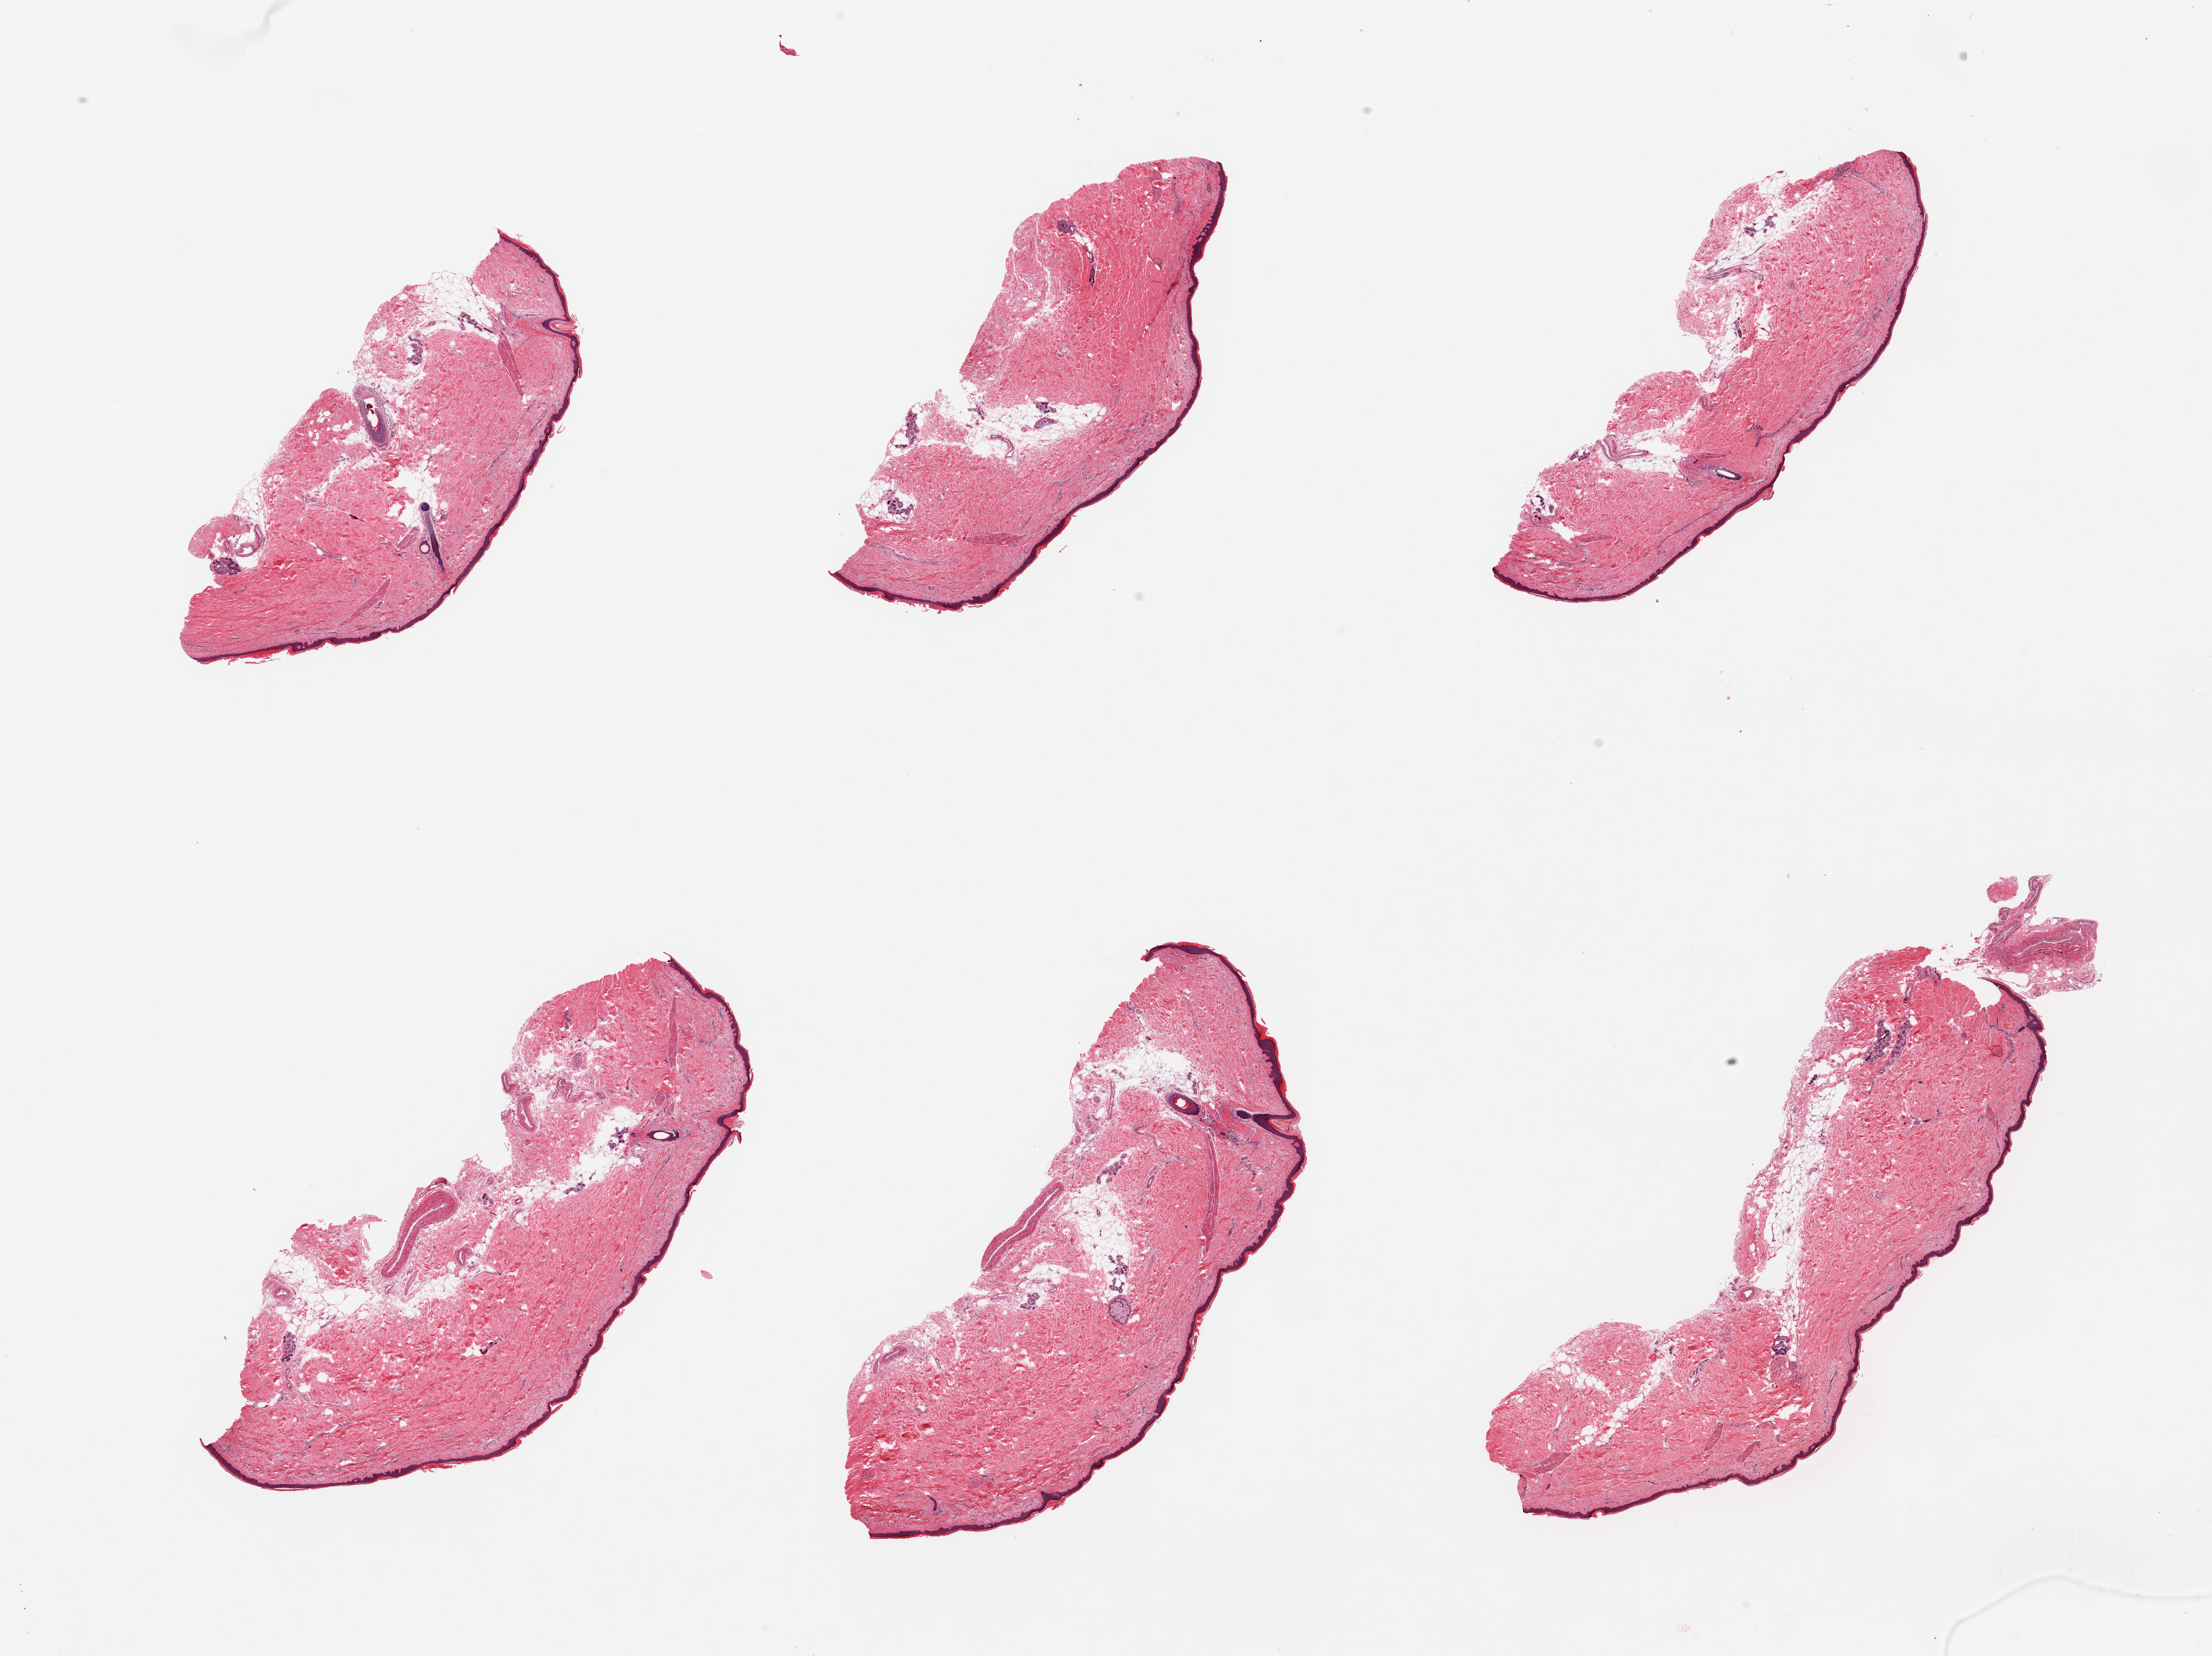
Digitized H&E-stained section, shown as a low-resolution overview of the whole scanned area (about 26.6 x 19.9 mm, acquisition: 20x scan); PAXgene-fixed, paraffin-embedded tissue; section of skin of lower leg (target tissue); donor tissue sample. Donor: female.
Review note (as recorded): 6 pieces; 10% dermal fat.